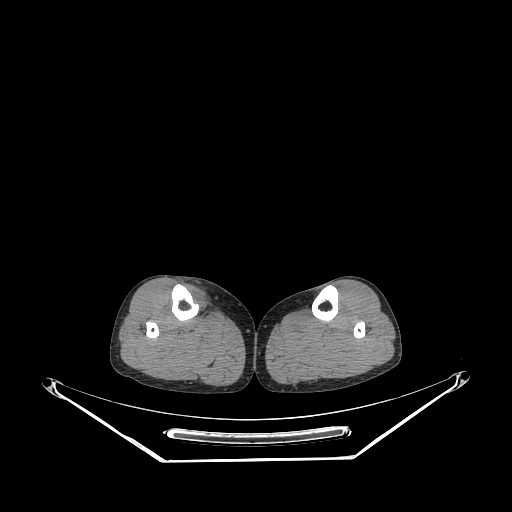
CT of an extremity soft-tissue mass (from a PET/CT study), one axial slice. Slice 135 of 267 in the series (ordered by position). Reconstruction kernel STANDARD. Soft-tissue window (W 400 / L 40 HU). 512 × 512 image matrix. Female patient. Case-level facts recorded for this patient, not image findings: histological type: undifferentiated – high grade; grade: high; site of the primary tumour: right thigh.
Annotated regions visible in this slice (expert contour drawn on MRI and transferred to this co-registered scan by the dataset authors):
- gross tumour volume (mass): box from (x=185, y=285) to (x=209, y=312) px